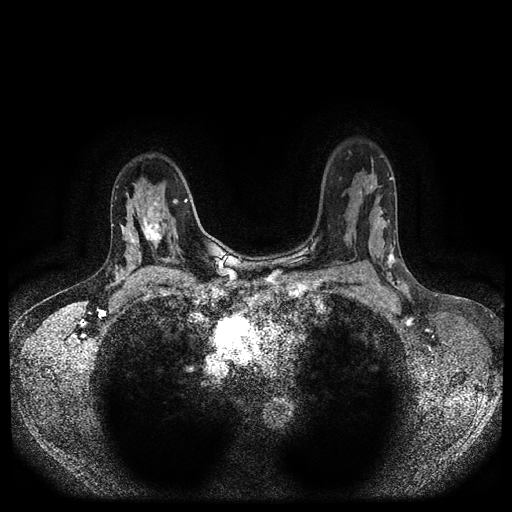
Breast MRI (dynamic contrast-enhanced, multi-phase), one axial slice. Slice 70 of 116 in the series (ordered by position). Dynamic contrast-enhanced series, time point 2 of 5 at this slice position (early post-contrast). 1.5 T. TE 2.6 ms, TR 5.4 ms. 512 × 512 image matrix. Female patient, age 47 years.
Outlined on this slice (semi-automatic segmentation, software-assisted and operator-edited):
- breast lesion (labelled 'tumour' in the annotation; benign lesions carry a separate 'benign' label): box from (x=140, y=196) to (x=166, y=248) px